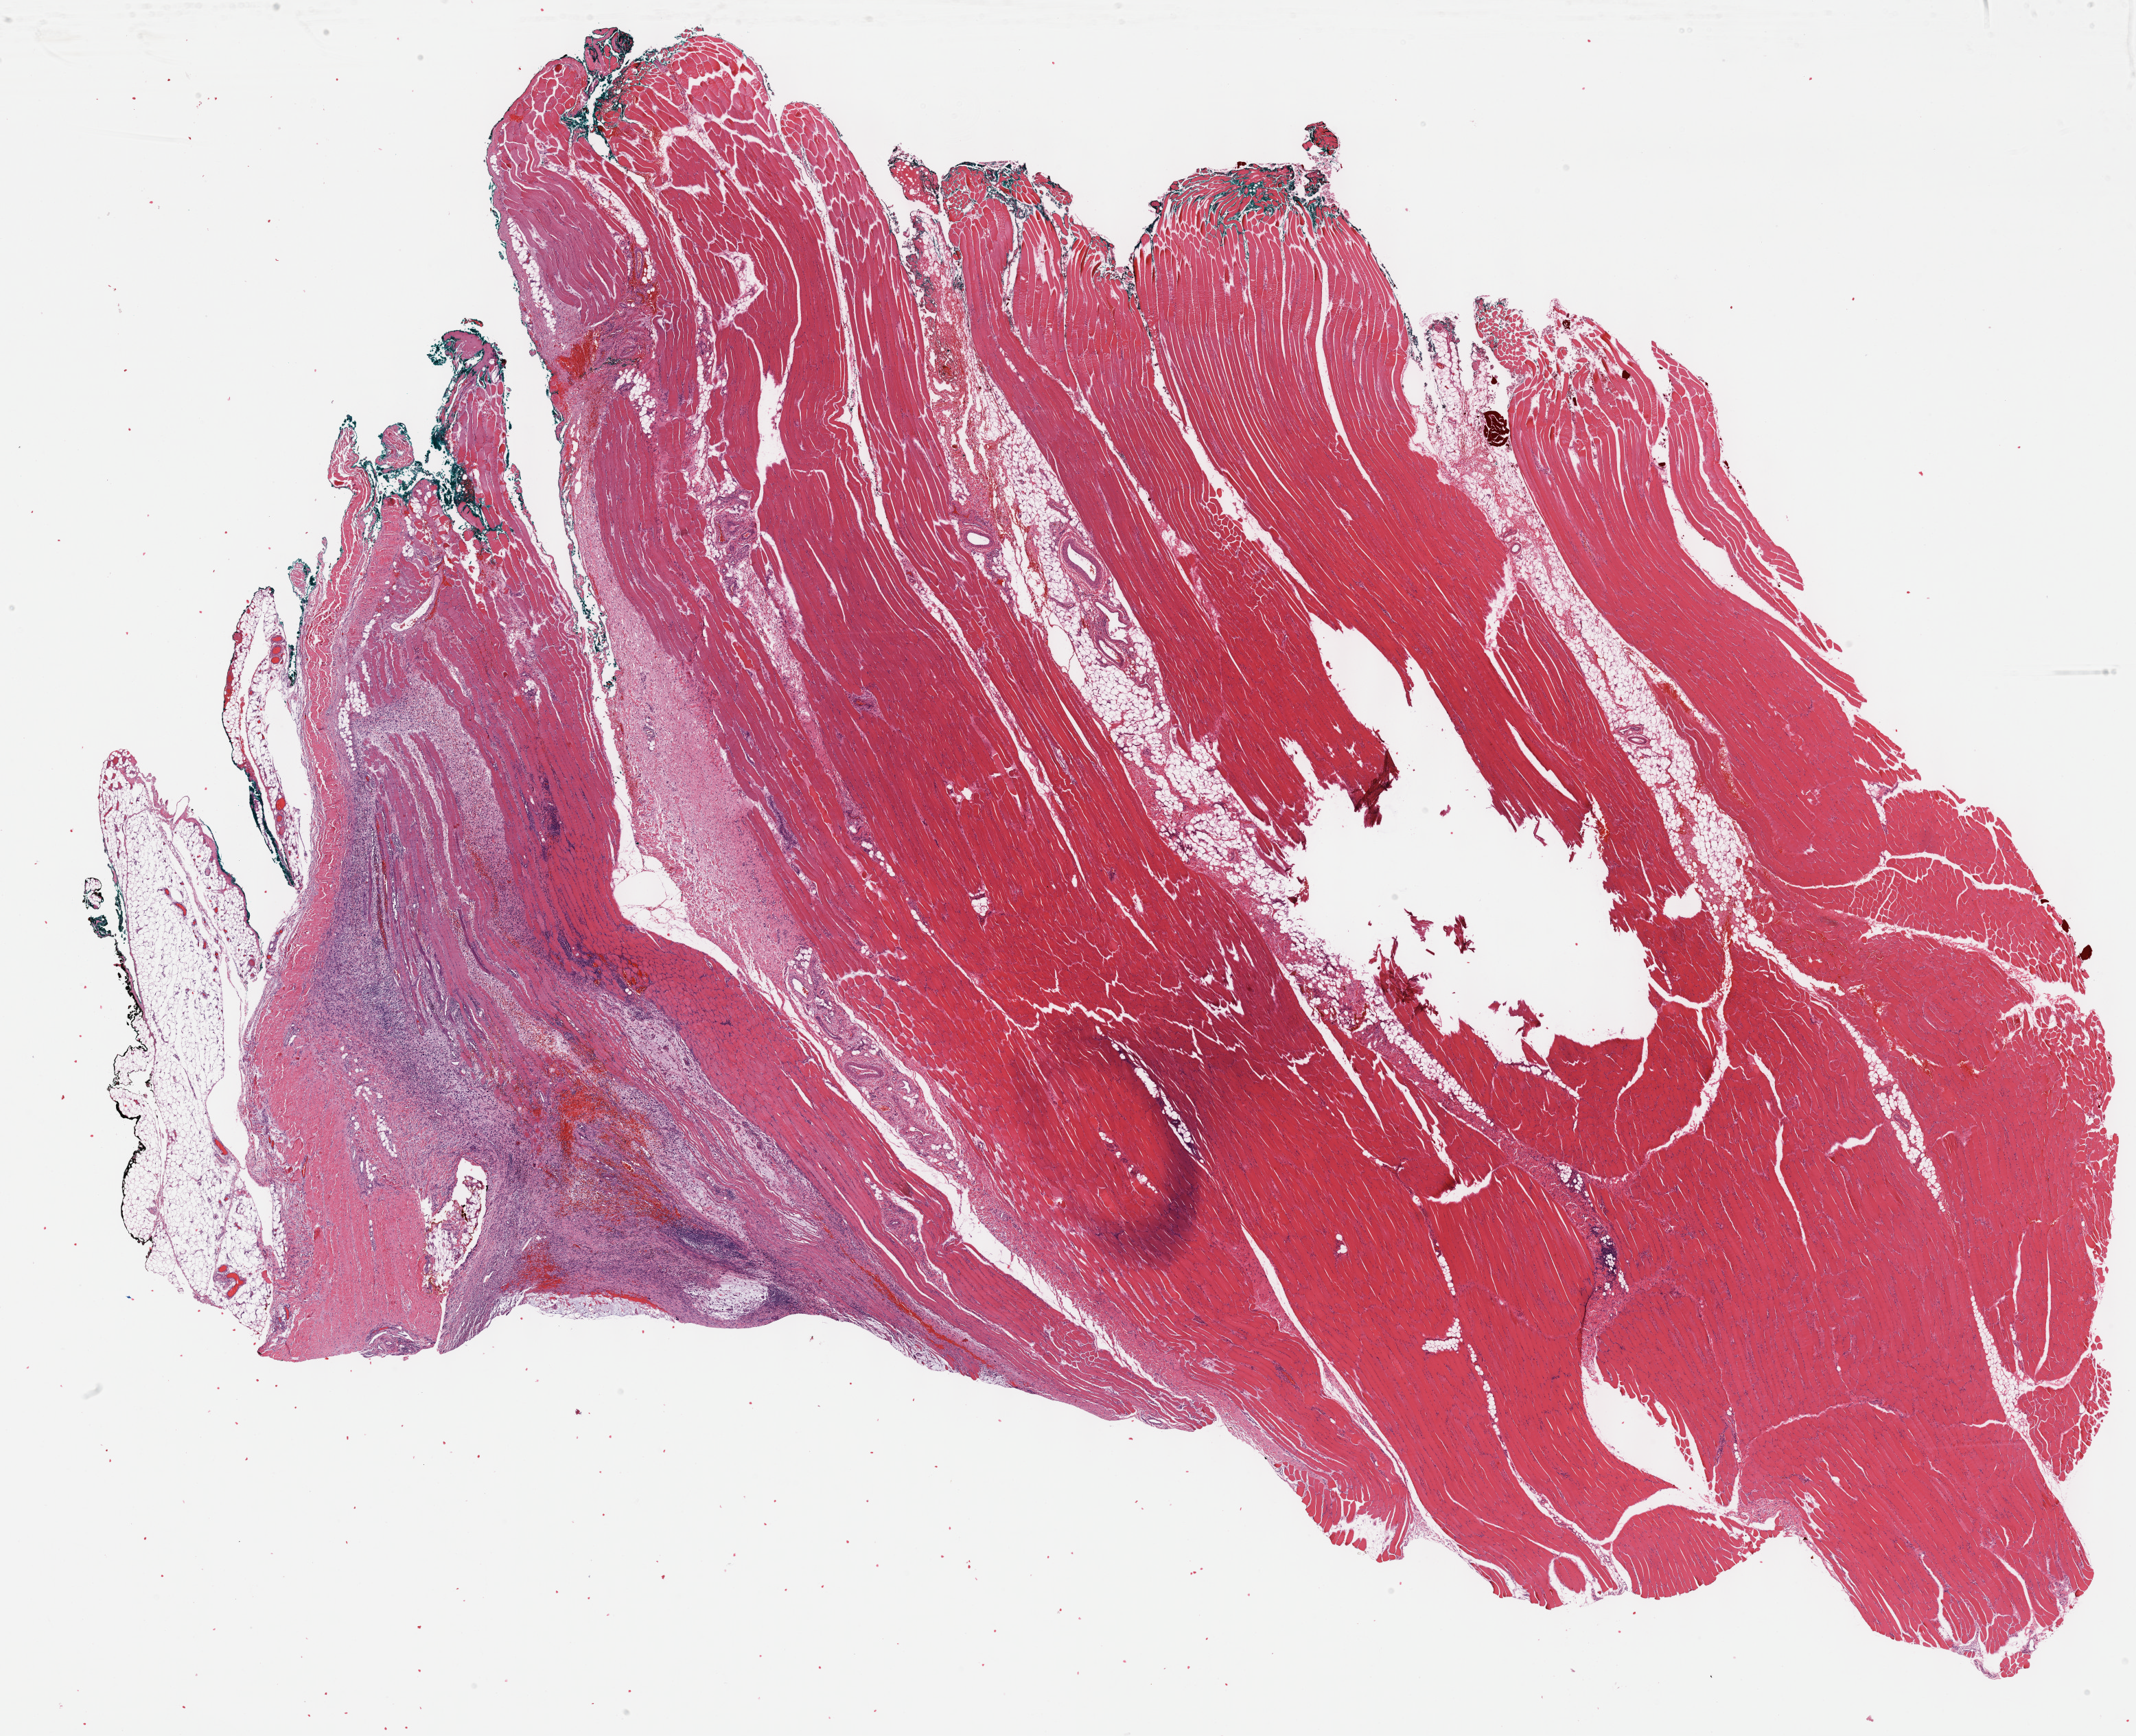
Whole-slide histology image, H&E-stained, low-resolution overview of the scanned area, about 25.2 x 20.5 mm (from a 40x scan); formalin-fixed paraffin-embedded (FFPE) diagnostic section; connective, subcutaneous and other soft tissues, primary tumour sample. Male patient; age at initial diagnosis 35 years.
Diagnosis: Fibromyxosarcoma (connective, subcutaneous and other soft tissues of lower limb and hip).